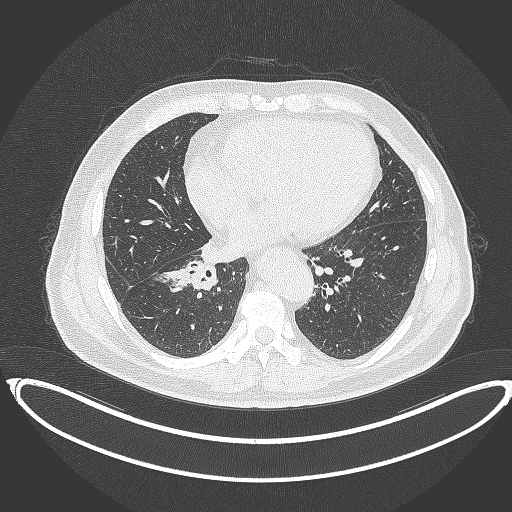
Chest CT, one axial slice. Reconstruction kernel B70f. Lung window (W 1500 / L -600 HU). 1 mm slice thickness. 512 × 512 image matrix, field of view 448 × 448 mm. Patient: male, 61 years. Case-level facts recorded for this patient, not image findings: clinical TNM (as recorded): T1b N1 M0.
Annotated regions visible in this slice (bounding box drawn by a radiologist):
- lung tumour (recorded histology: squamous cell carcinoma): bounding box (x1, y1, x2, y2) in pixels: (157, 257, 219, 297)